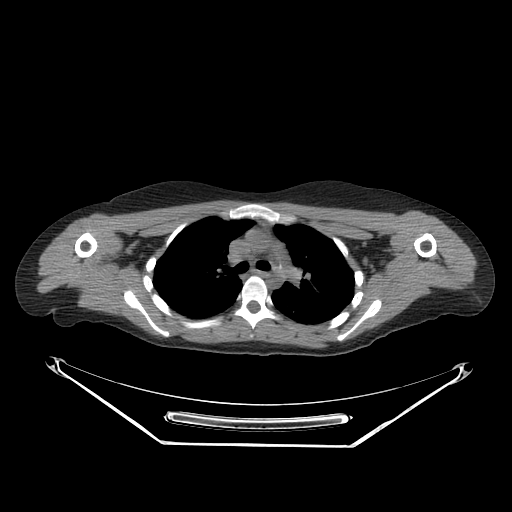
CT of an extremity soft-tissue mass (from a PET/CT study), one axial slice; slice 201 of 267 in the series (ordered by position); soft-tissue window (W 400 / L 40 HU); 3.75 mm slice thickness; 512 × 512 image matrix, field of view 500 × 500 mm. Female patient. Case-level facts recorded for this patient, not image findings: histological type: malignant fibrous histiocytoma; grade: low; site of the primary tumour: left arm.
Annotated regions visible in this slice (expert contour drawn on MRI and transferred to this co-registered scan by the dataset authors):
- gross tumour volume (mass): bounding box <429,253,455,280> (left, top, right, bottom; pixels)